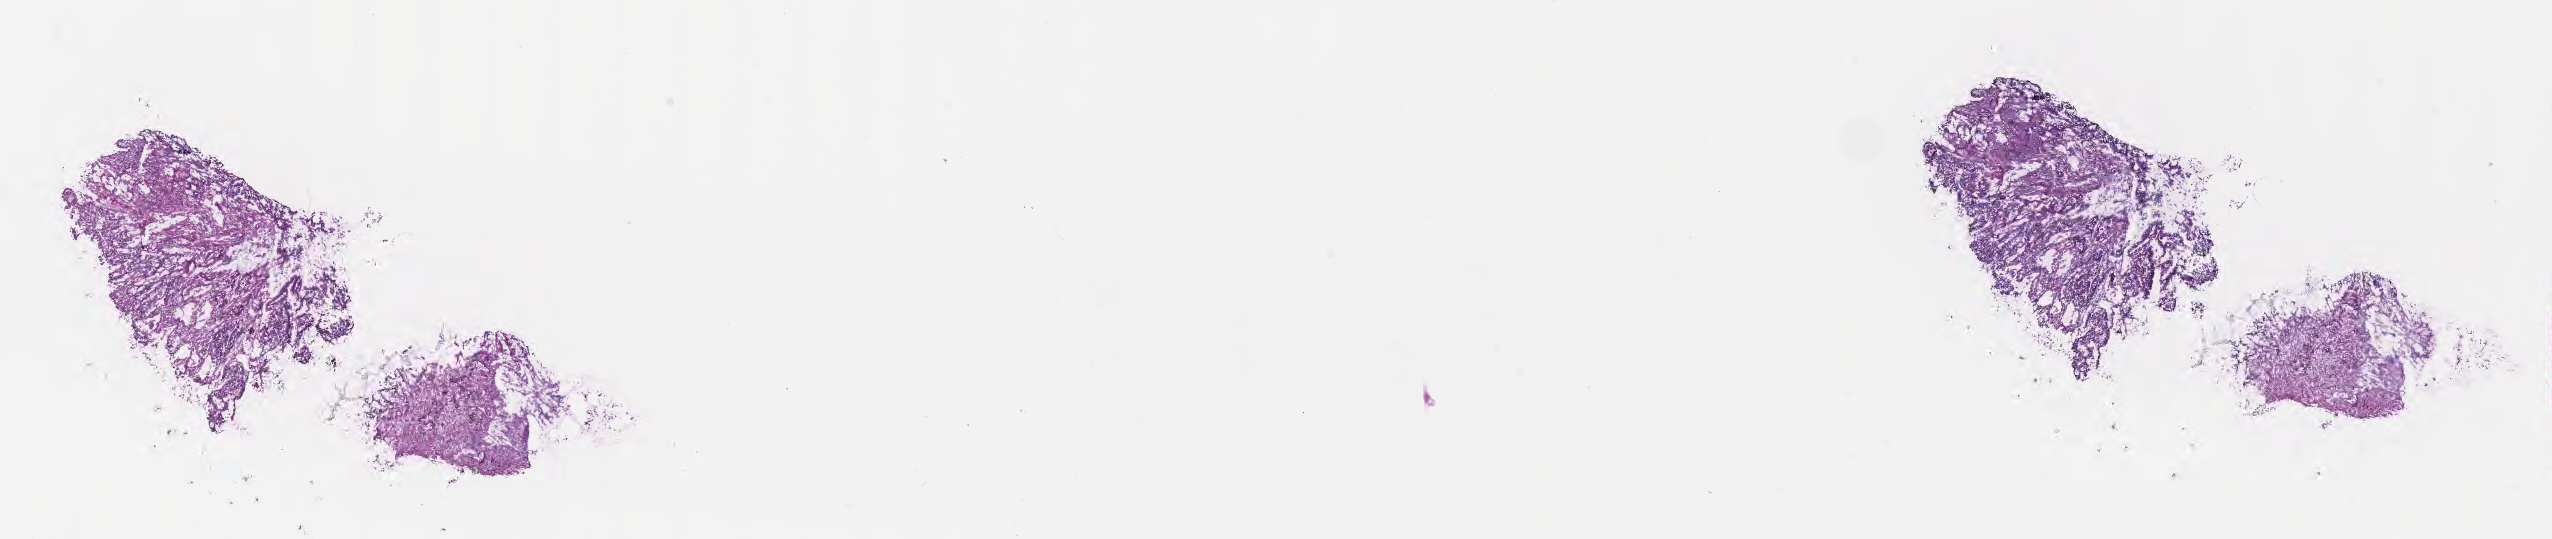
Whole-slide image, hematoxylin and eosin (H&E) stain, a low-resolution overview of the entire scanned area, about 20.6 x 4.4 mm; frozen section; primary tumor; anatomic site: sigmoid colon. Patient: male, age at initial diagnosis 51 years. Tumor grade: G2 (moderately differentiated). Pathologist review of this section (percent, as recorded): tumor cells 80%, tumor nuclei 80%, stromal cells 18%, necrosis 2%, normal cells 0%. Inflammatory infiltration, as recorded: lymphocyte infiltration 4%, monocyte infiltration 2%, neutrophil infiltration 7%.
Diagnosis: Adenocarcinoma, NOS. AJCC pathologic stage: Stage IIIA.